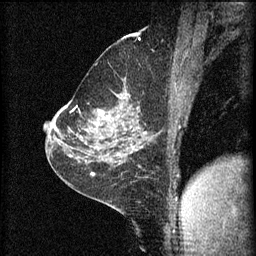
Breast MRI (dynamic contrast-enhanced), one sagittal slice. Position 39 of 60 along the scan axis. 3 images stored at this slice position (order not interpretable as contrast timing). 1.5 T. TE 4.2 ms, TR 8.2 ms. 256 × 256 image matrix, field of view 180 × 180 mm. Female patient, age 59 years.
Structures marked on this image (semi-automatically segmented with operator editing):
- analysis volume of interest (the breast-tissue region the enhancement analysis was run in; not a lesion): bounding box [x1, y1, x2, y2] px = [78, 92, 137, 135]
- tumour enhancement mask (voxels above the 70 % enhancement threshold inside the analysis volume of interest): [96, 110, 101, 127]